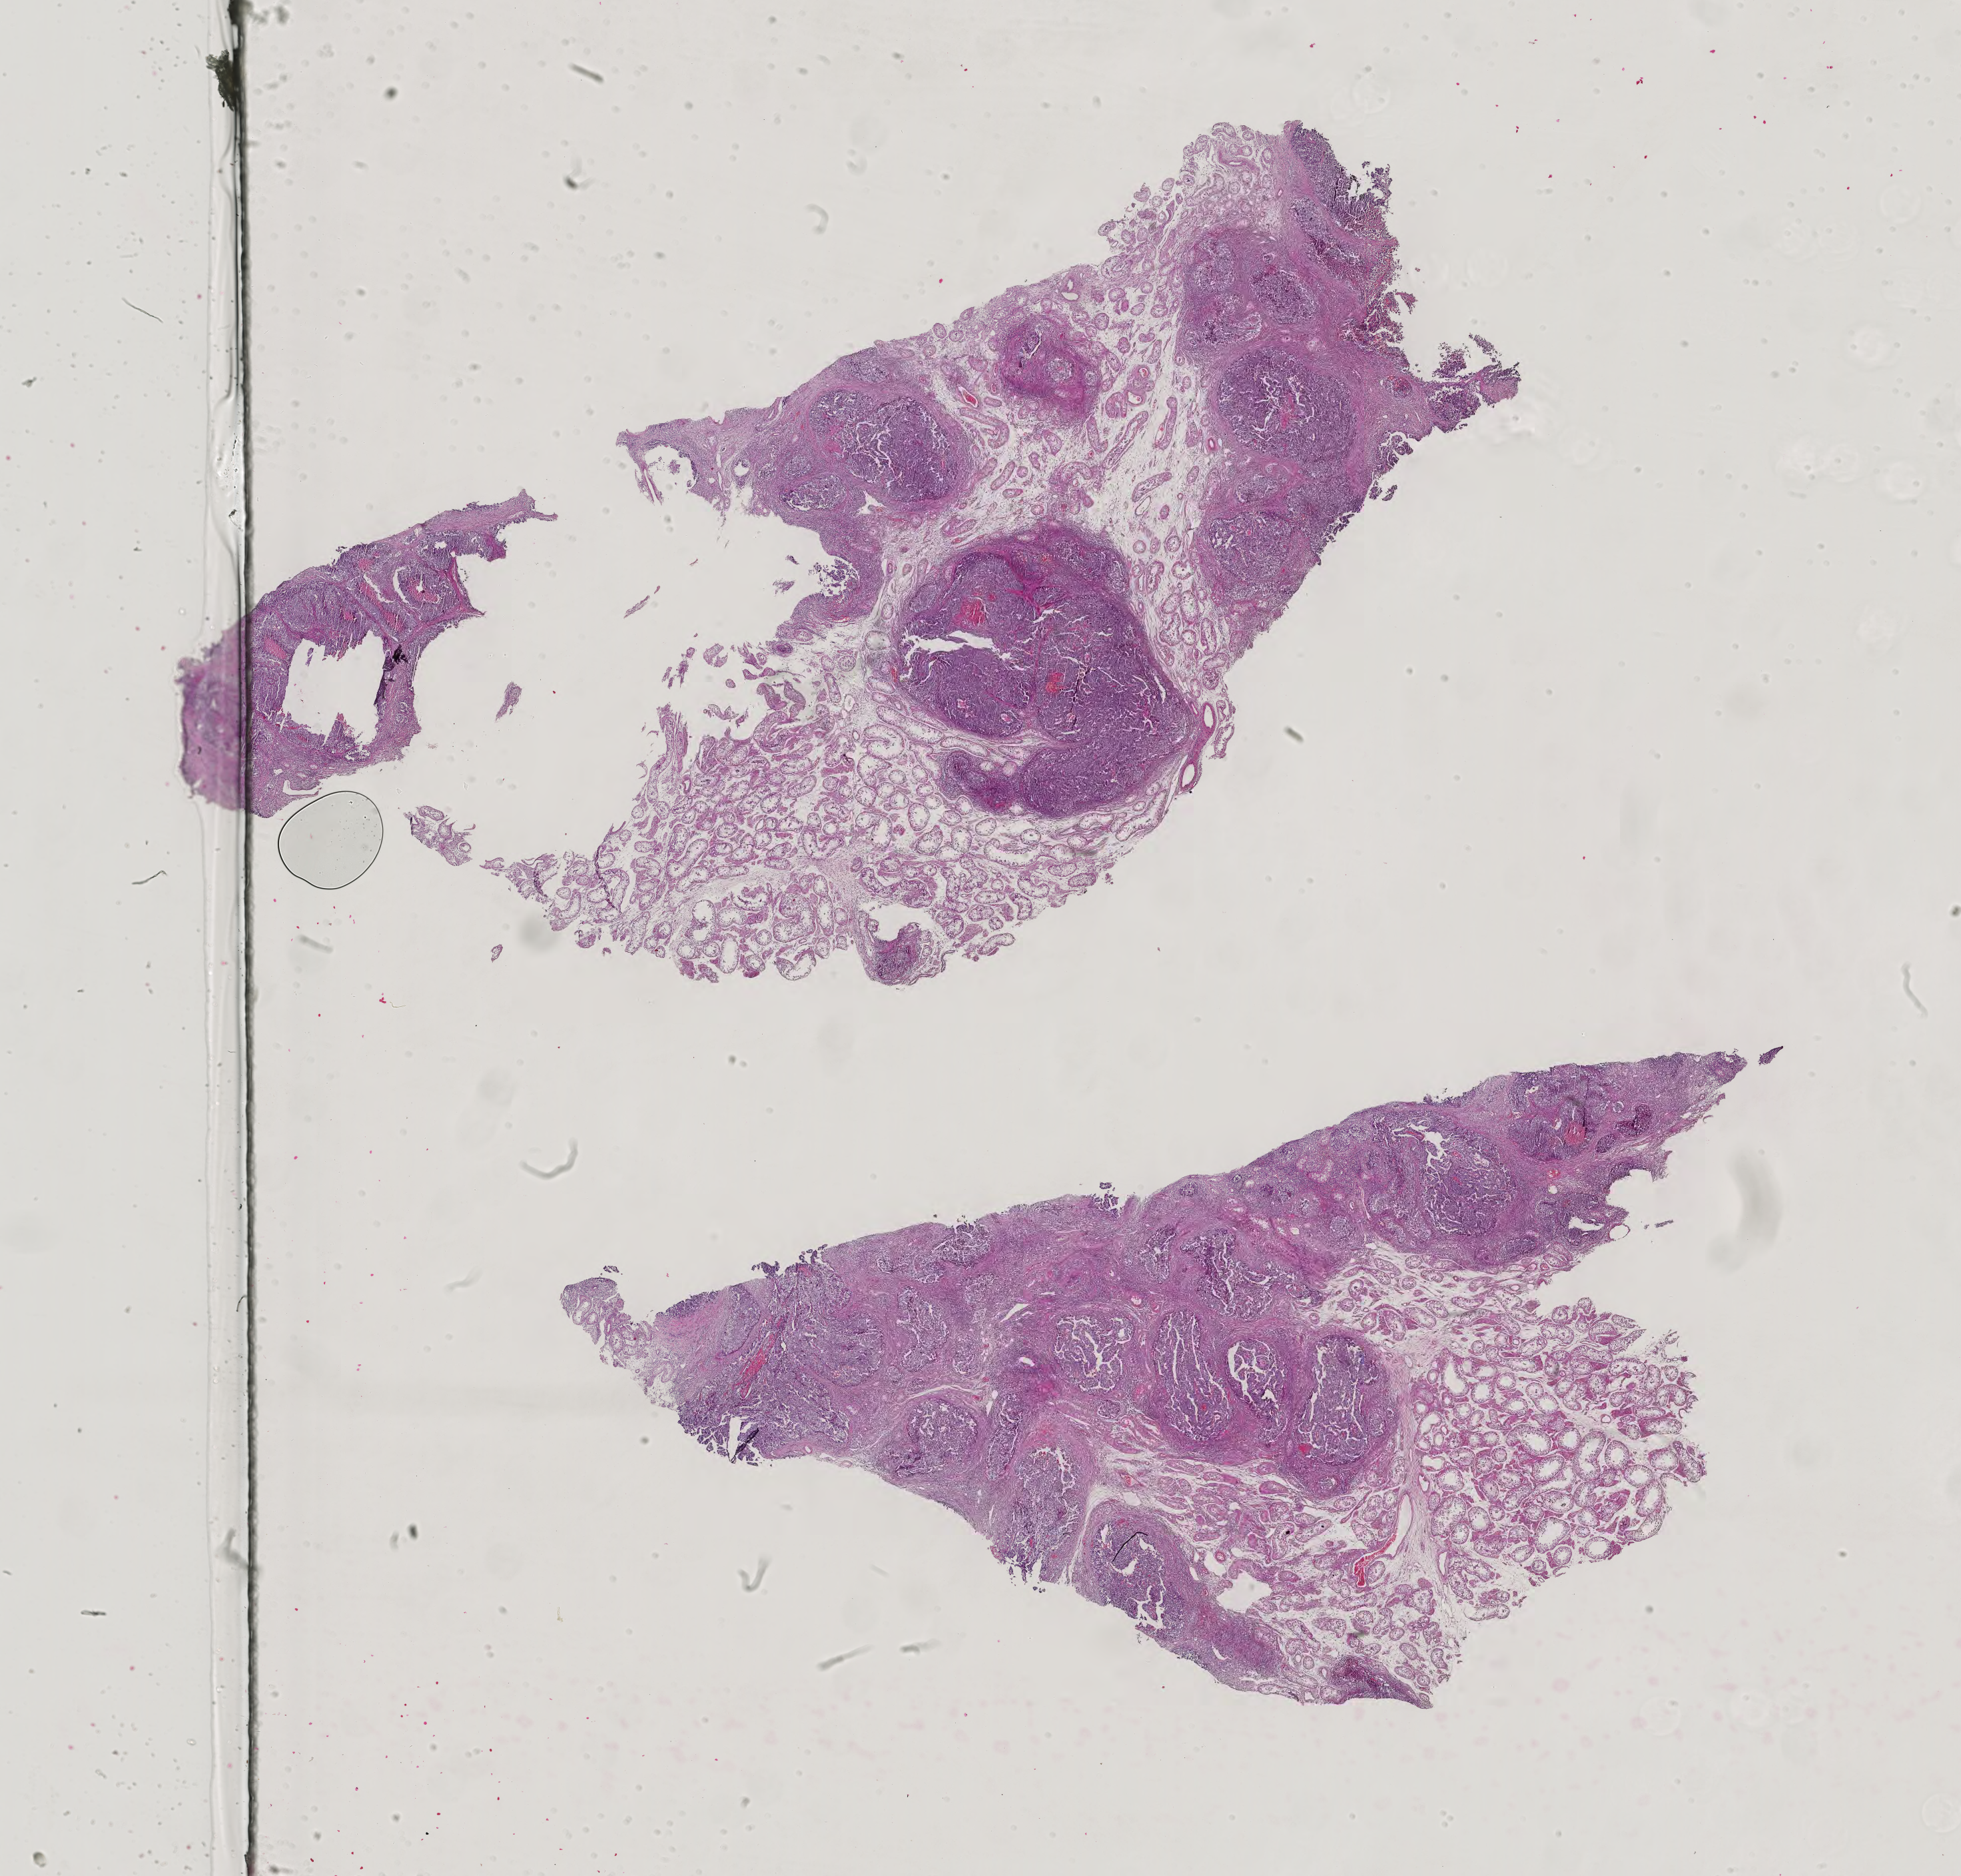
H&E-stained whole-slide image, whole scanned area (about 21.5 x 20.5 mm) shown as a low-resolution overview; FFPE section; testis, primary tumour sample. Patient: male, age at initial diagnosis 23 years.
AJCC pathologic stage: IS (7th edition). Histologic diagnosis: Mixed germ cell tumor.